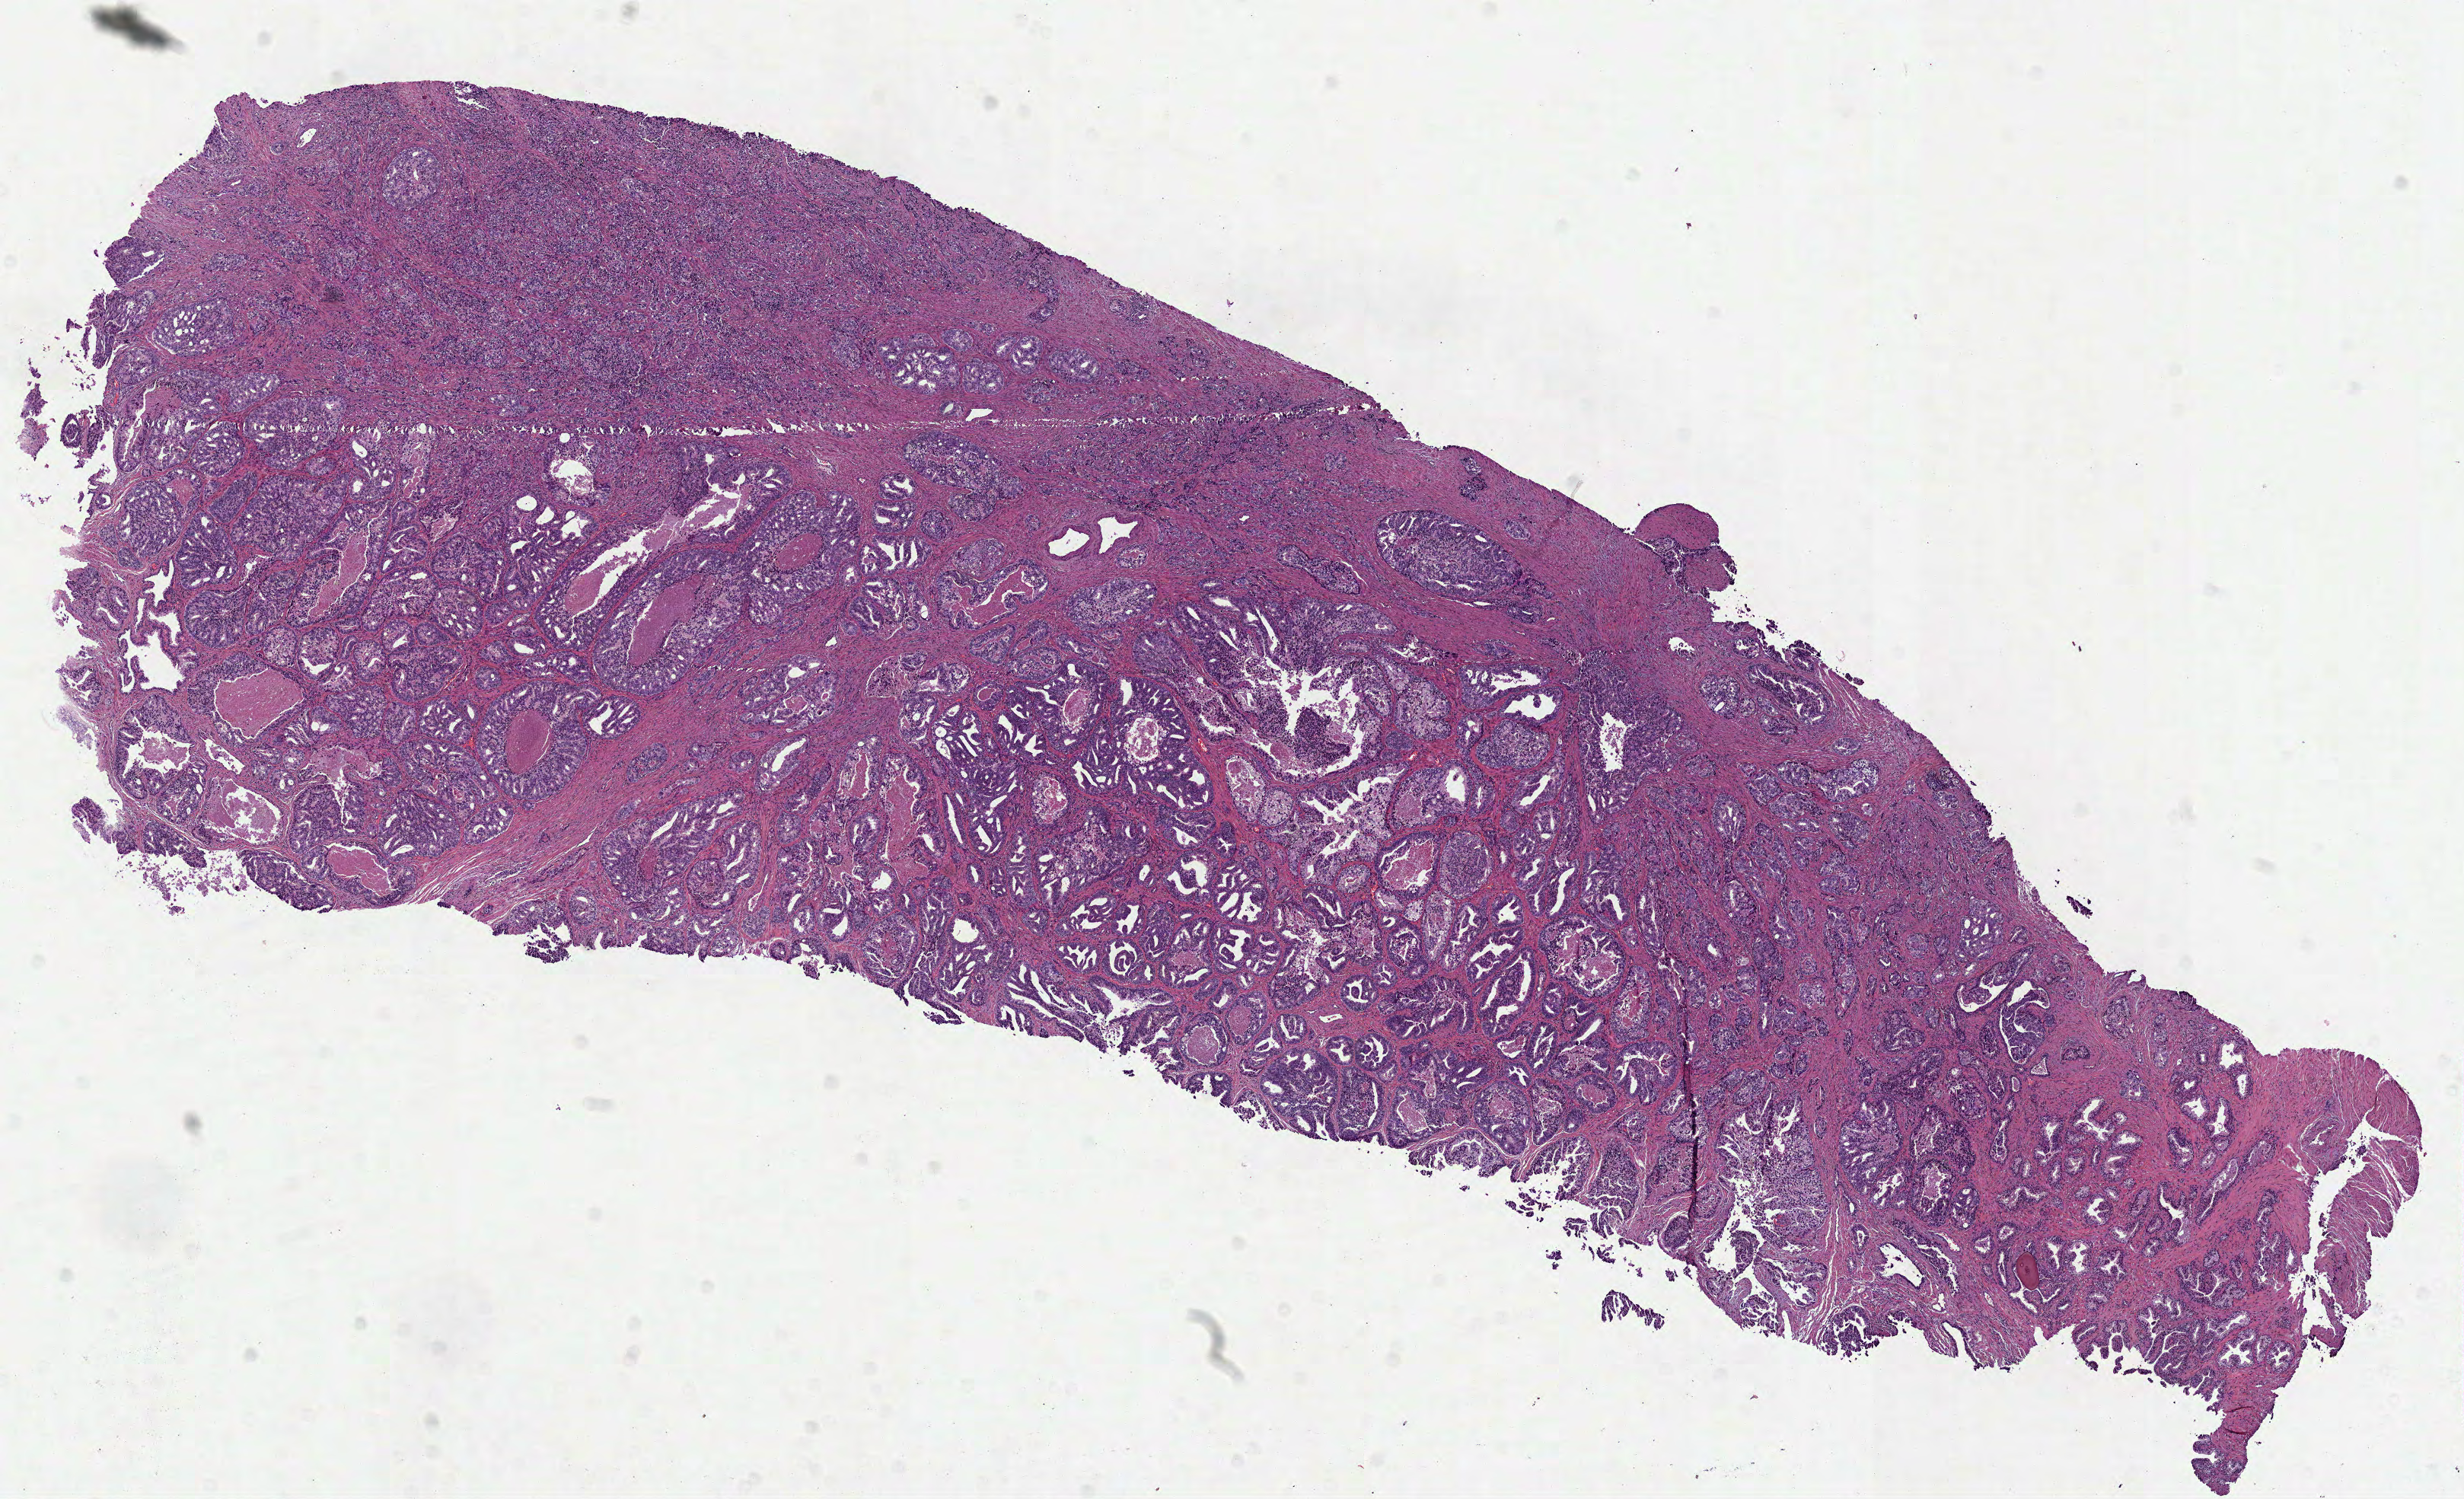
H&E-stained whole-slide image, low-resolution overview of the scanned area, about 13.1 x 7.9 mm (from a 40x scan), FFPE section, primary tumour sample from the prostate. Patient: male, age at initial diagnosis 53 years. Gleason score: 9 (4+5).
Laterality: bilateral. Diagnosis: Acinar cell carcinoma (prostate gland).